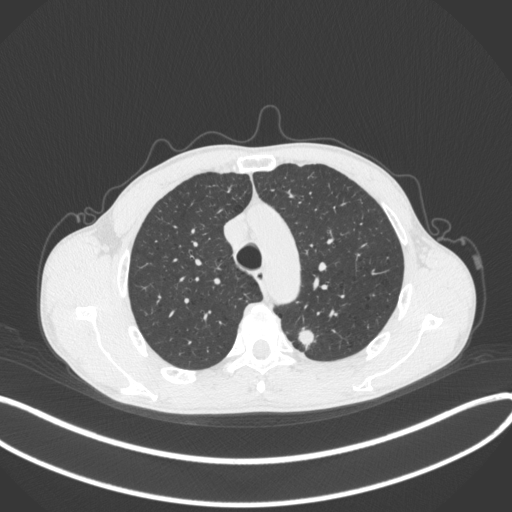
Chest CT, one axial slice; slice 299 of 429 in the series (ordered by position); reconstruction kernel B31f; lung window (W 1500 / L -600 HU); 1 mm slice thickness; 512 × 512 image matrix, field of view 400 × 400 mm. Patient: male, 51 years. Case-level facts recorded for this patient, not image findings: clinical TNM (as recorded): T2a N1 M1.
Structures marked on this image (rectangle marked by the reading radiologist):
- lung tumour (recorded histology: adenocarcinoma): bounding box [x1, y1, x2, y2] px = [293, 321, 317, 354]